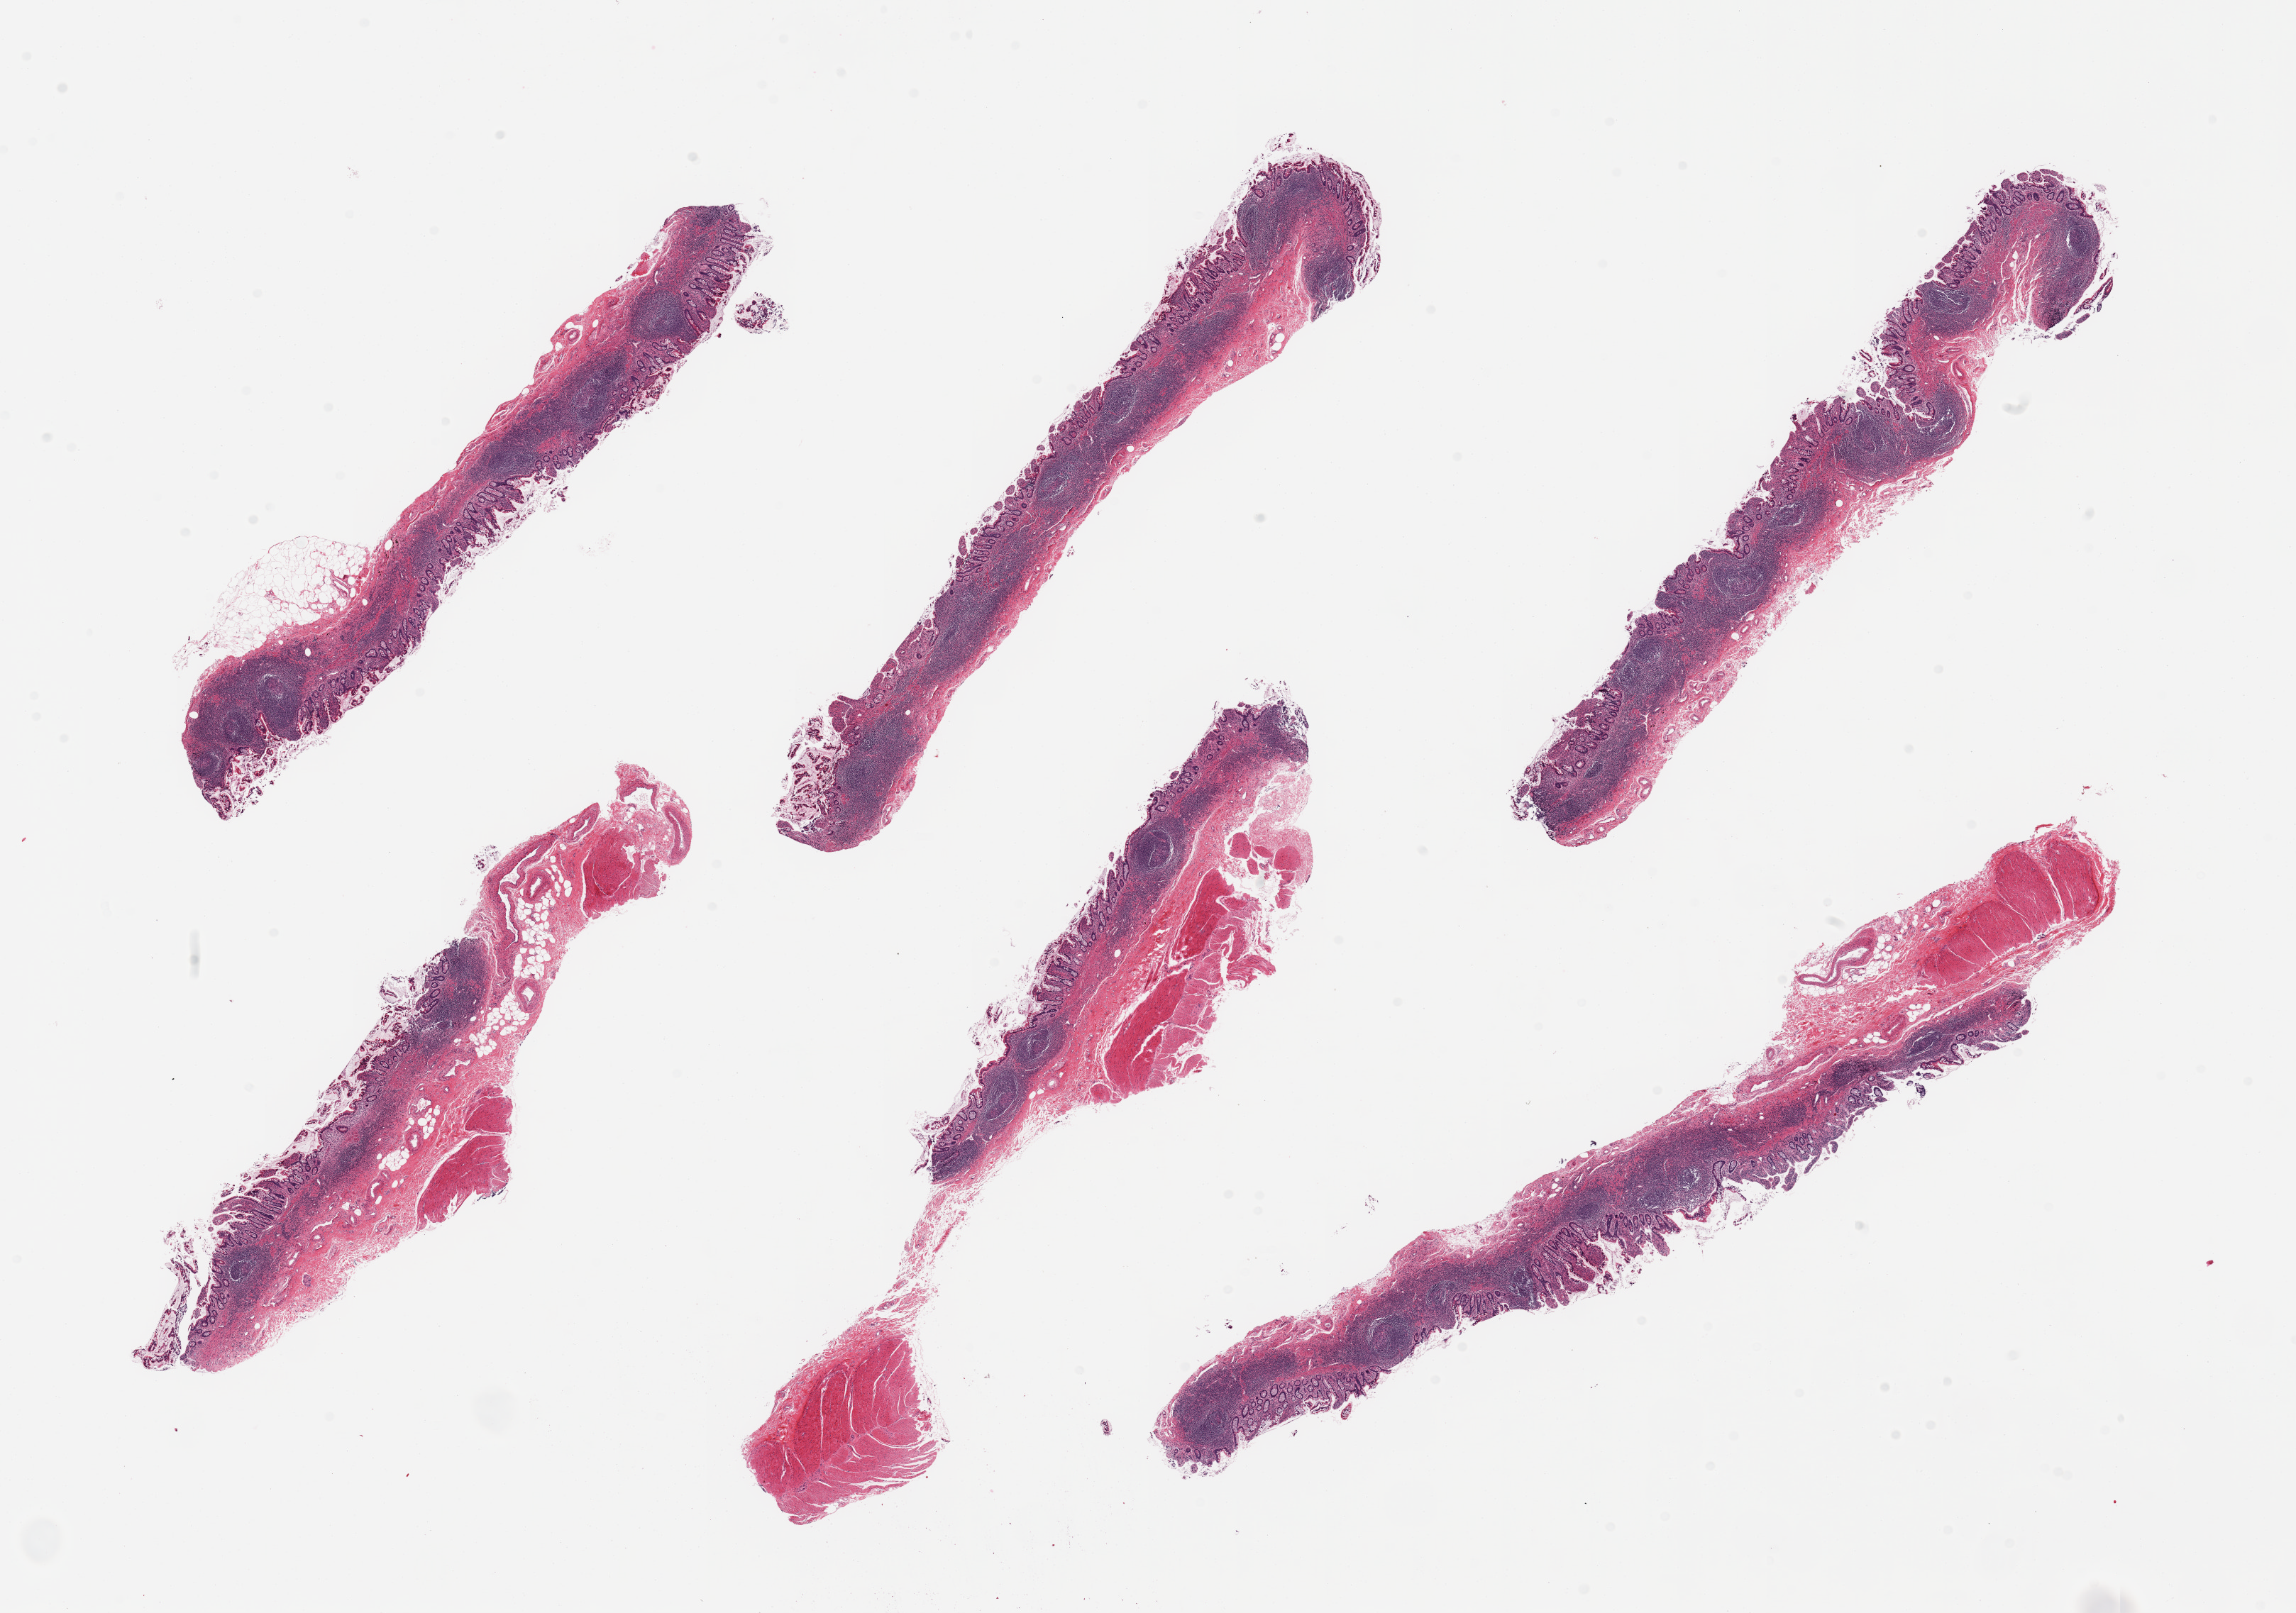
Whole-slide image, haematoxylin and eosin stain, shown as a low-resolution overview of the whole scanned area (about 25.6 x 18.0 mm, from a 20x scan), PAXgene-fixed, paraffin-embedded tissue, target tissue: ileum, tissue donor sample. Donor: male.
- review note (as recorded): 6 pieces; all pieces contain lymphoid nodulles